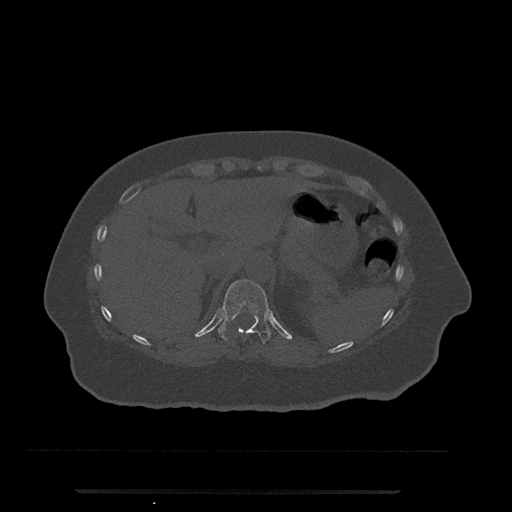
CT including the spine, one axial slice. Slice 235 of 797 in the series (ordered by position). Reconstruction kernel Br40s/3. Bone window (W 1800 / L 400 HU). 0.5 mm slice thickness. 512 × 512 image matrix, field of view 440 × 440 mm. Patient: female, 51 years. From the clinical record (not read from this slice): primary cancer: neuro; vertebrae with lytic lesions (as recorded): T8.
Annotated regions visible in this slice (semi-automatic segmentation, software-assisted and operator-edited):
- T11 vertebra: bounding box (x1, y1, x2, y2) in pixels: (218, 279, 271, 345)